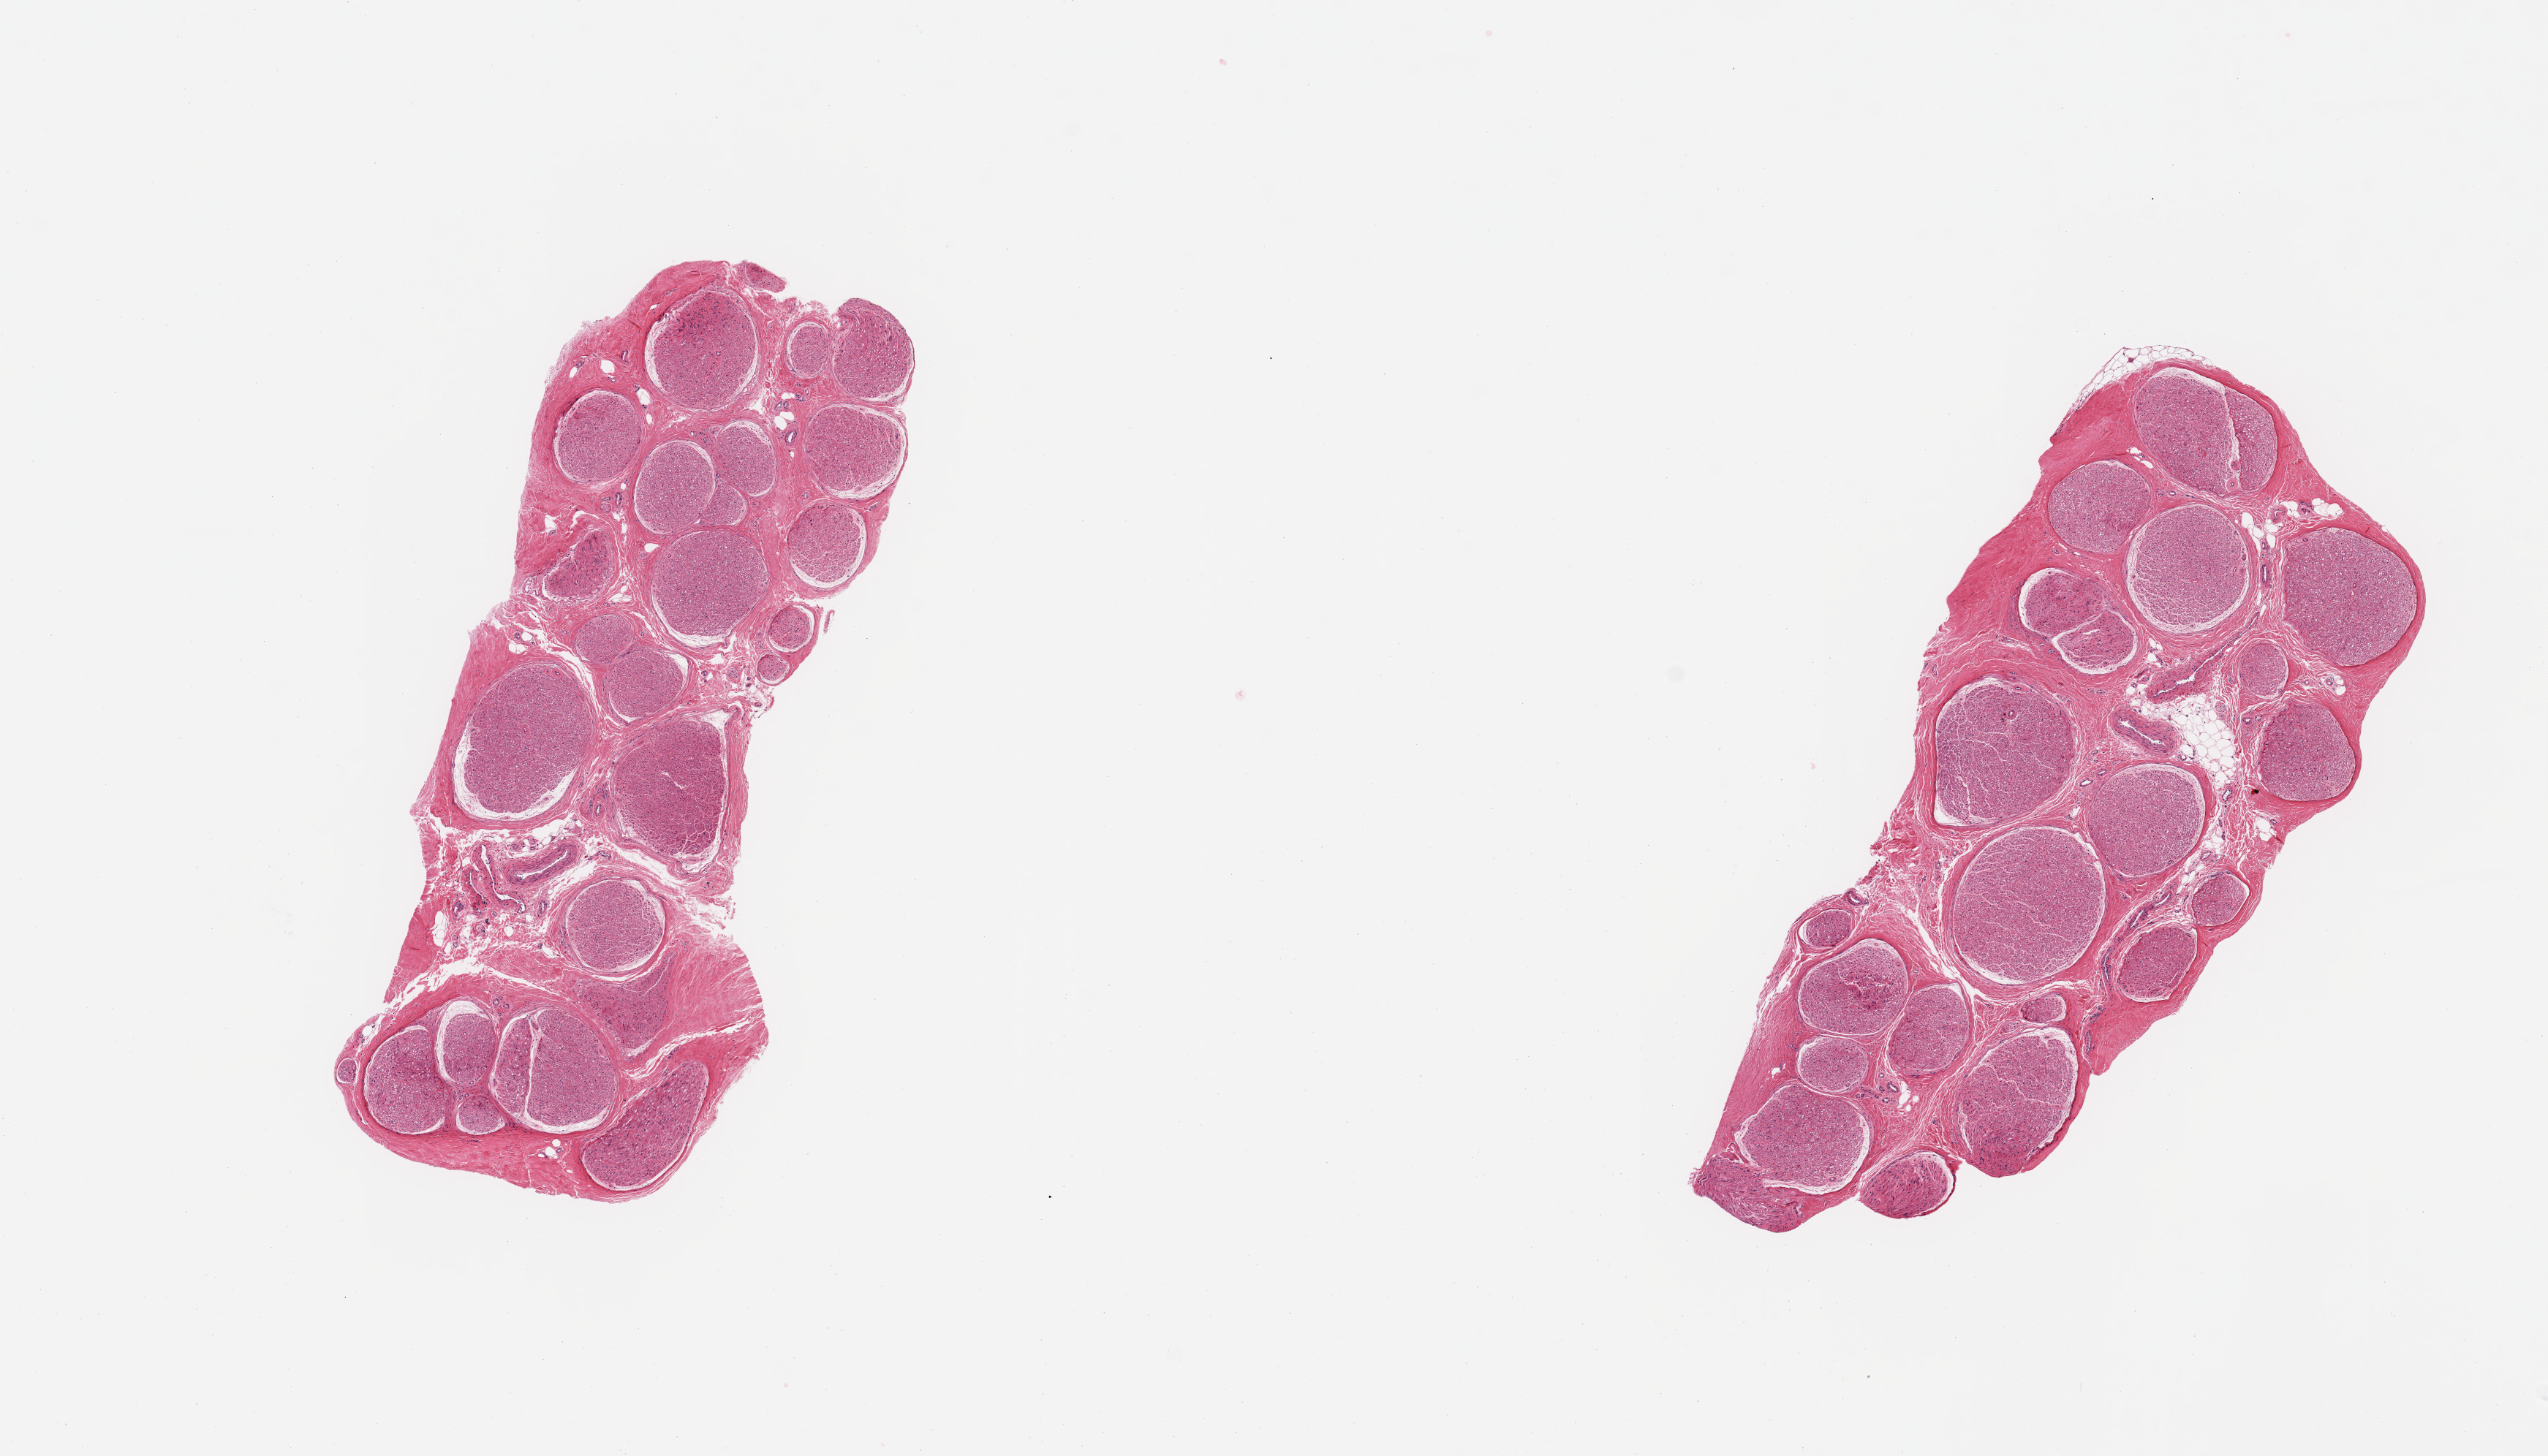
Digitized hematoxylin and eosin (H&E)-stained section — whole scanned area (about 13.8 x 7.9 mm, acquisition: 20x scan) shown as a low-resolution overview; PAXgene-fixed paraffin-embedded (PFPE) section; section of tibial nerve (target tissue); tissue donor sample. Male donor.
Reviewer comment on this tissue sample: 2 pieces; essentially well trimmed.